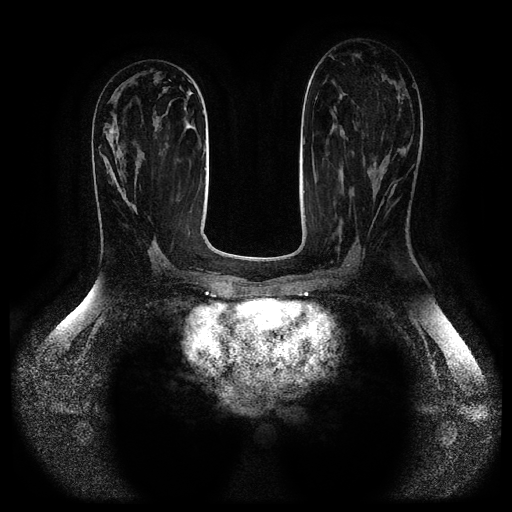
Breast MRI (dynamic contrast-enhanced, multi-phase), one axial slice. Position 43 of 116 along the scan axis. Dynamic contrast-enhanced series, time point 2 of 5 at this slice position (early post-contrast). 1.5 T. TE 2.6 ms, TR 5.2 ms. 2 mm slice thickness. 512 × 512 image matrix. Female patient, age 44 years.
Outlined on this slice (semi-automatic segmentation, software-assisted and operator-edited):
- breast lesion (labelled benign in the annotation): bounding box [x1, y1, x2, y2] px = [99, 129, 138, 208]